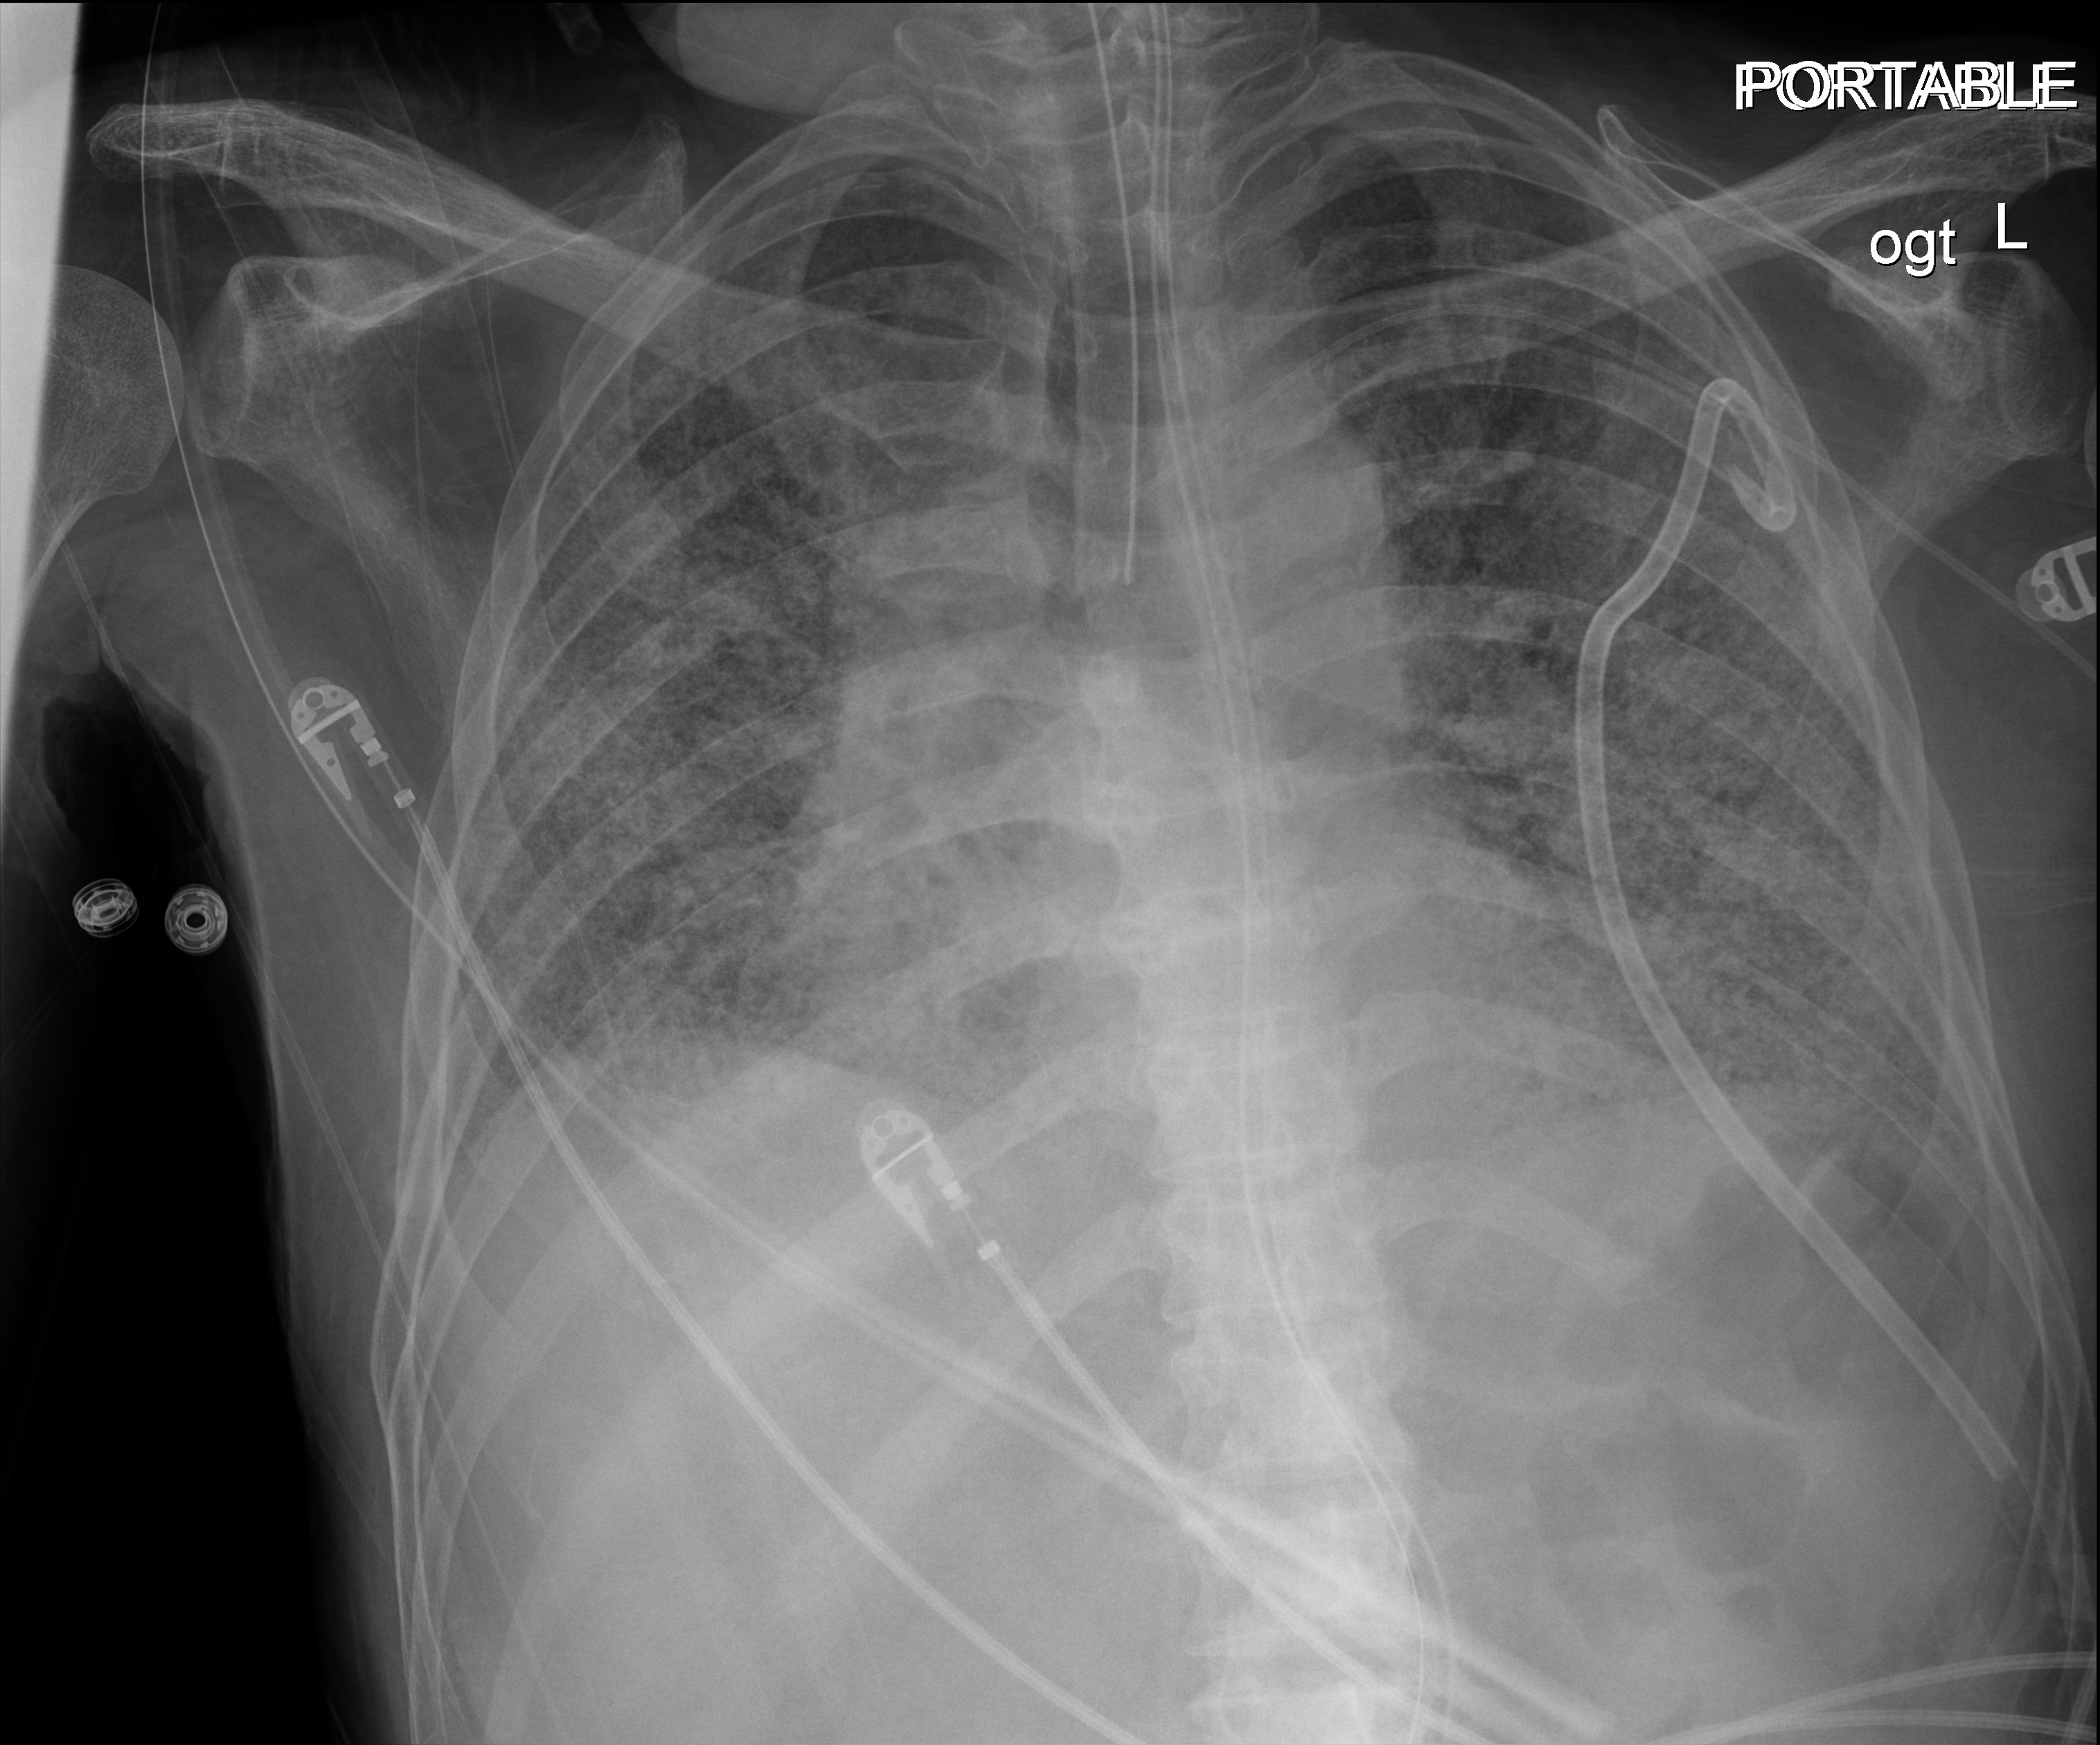
Chest X-ray, anteroposterior (AP) projection. Male patient hospitalised with COVID-19, age 60–74 years.
Admission-level facts for this patient (not findings on this image; timing relative to this image not recorded): admitted to intensive care during this hospital stay: yes; length of hospital stay: 54 days; mechanically ventilated during this hospital stay: yes.